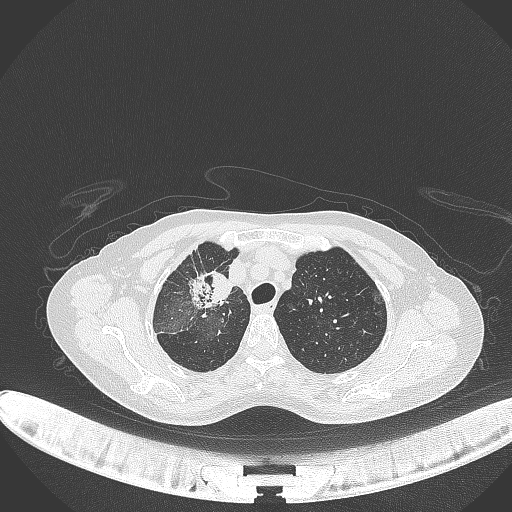
Chest CT, one axial slice. Position 256 of 284 along the scan axis. Lung window (W 1500 / L -600 HU). 1 mm slice thickness. 512 × 512 image matrix, field of view 400 × 400 mm. Patient: female, 59 years. Case-level facts recorded for this patient, not image findings: clinical TNM (as recorded): T3 N0 M0.
Annotated regions visible in this slice (rectangle marked by the reading radiologist):
- lung tumour (recorded histology: adenocarcinoma): bounding box <187,264,233,308> (left, top, right, bottom; pixels)